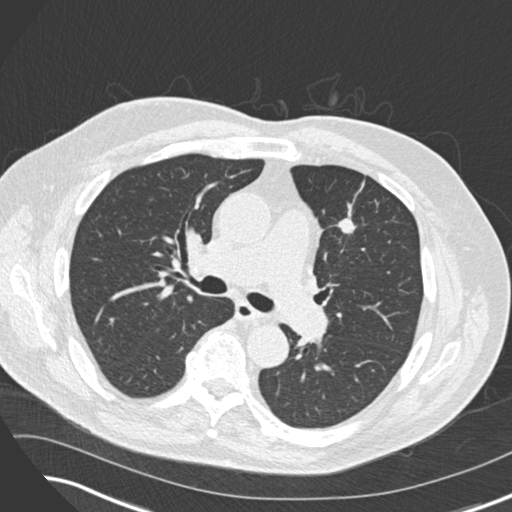
Axial slice from a low-dose chest CT screening exam. Third annual screen. Lung window (W 1500 / L -600 HU). 2 mm slice thickness. 120 kVp. Male participant, aged 74 years at enrolment. Former smoker at enrolment.
Expert-annotated lung lesion, box from (x=319, y=198) to (x=375, y=248) px. Screening reader's record for this exam (one nodule recorded; not confirmed to be the boxed lesion): non-calcified nodule or mass ≥4 mm, left upper lobe, 12 × 10 mm, spiculated (stellate) margins, soft tissue attenuation, pre-existing on the prior screen: yes; interval growth: yes. Lung cancer was diagnosed 349 days after this screen: adenocarcinoma, NOS, left upper lobe, poorly differentiated (G3), stage IIIA (AJCC 6th edition), 27 mm at pathology.